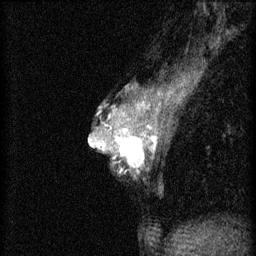
Breast MRI (dynamic contrast-enhanced), one sagittal slice. Position 32 of 46 along the scan axis. 3 images stored at this slice position (order not interpretable as contrast timing). 1.5 T. TE 4.2 ms, TR 8.2 ms. 256 × 256 image matrix. Female patient, age 44 years.
Structures marked on this image (semi-automatically segmented with operator editing):
- analysis volume of interest (the breast-tissue region the enhancement analysis was run in; not a lesion): bounding box <110,128,156,175> (left, top, right, bottom; pixels)
- tumour enhancement mask (voxels above the 70 % enhancement threshold inside the analysis volume of interest): <110,128,156,173>